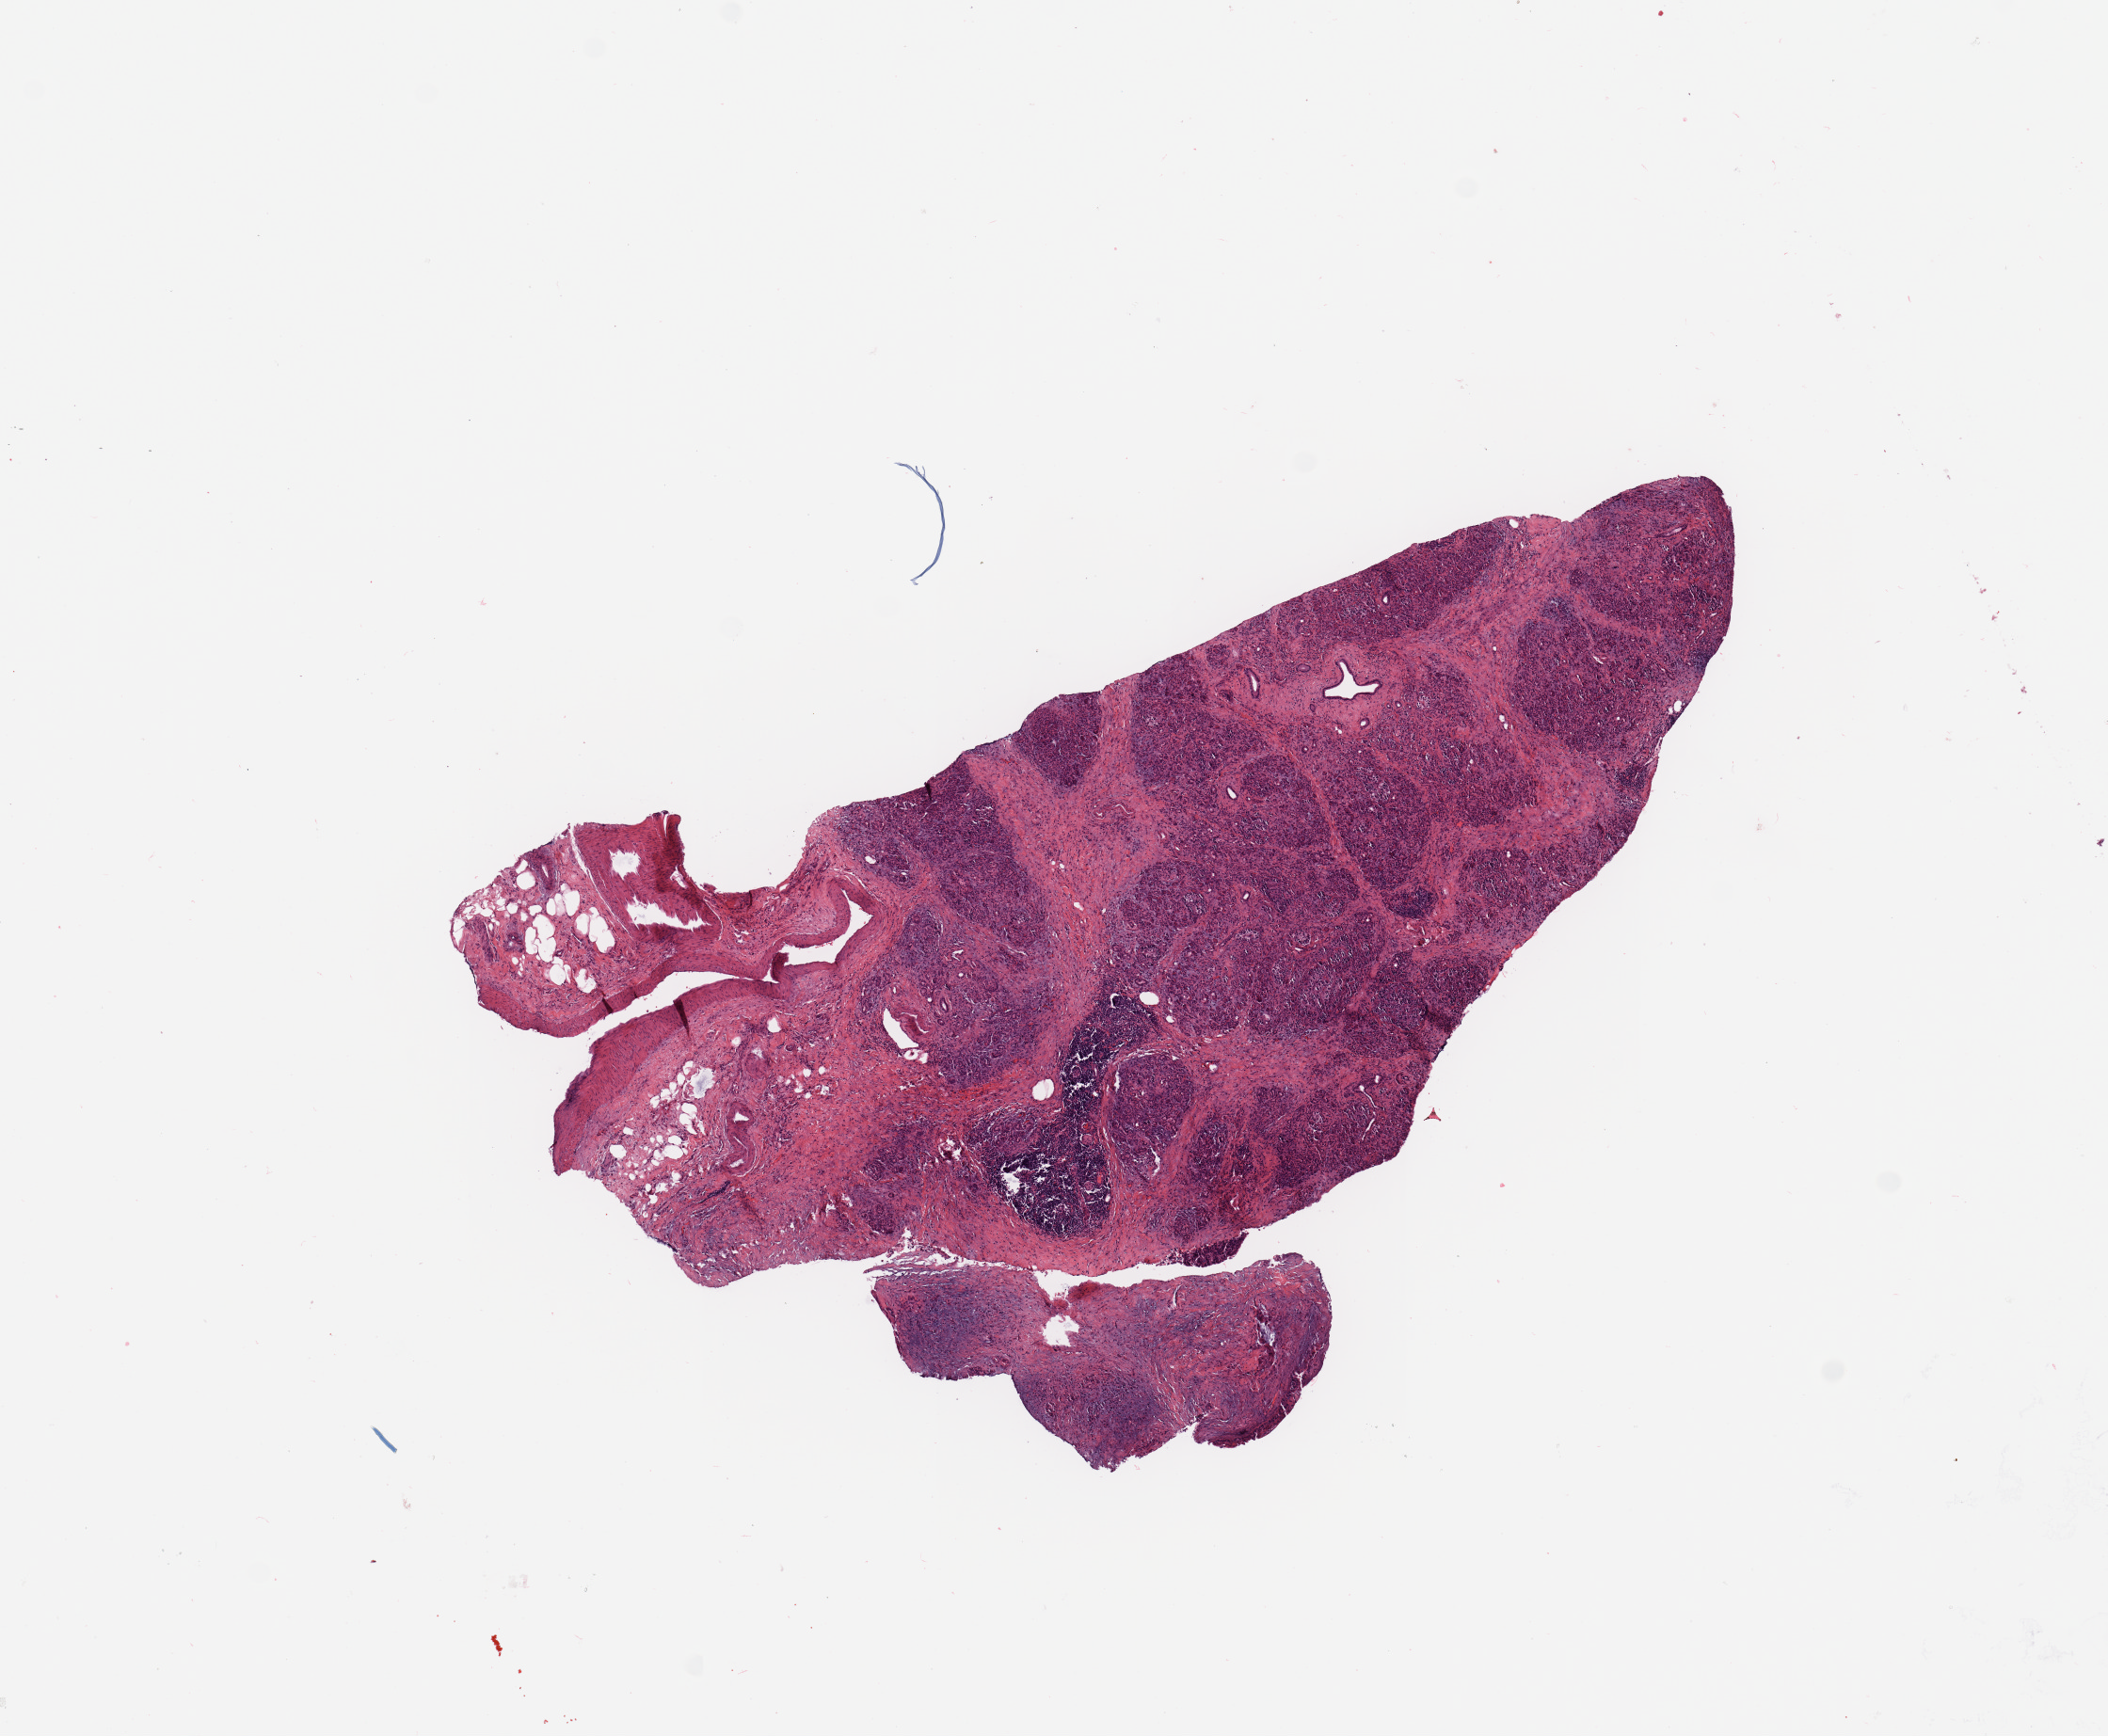
Digitized H&E tissue section (whole slide), shown as a low-resolution overview of the whole scanned area (about 8.9 x 7.3 mm, acquisition: 20x scan); tumour tissue sample, pancreas. 66-year-old male patient. Histologic grade: G3 (poorly differentiated).
AJCC pathologic stage: IIA. Diagnosis: Infiltrating duct carcinoma, NOS. Primary tumour site (as recorded): head.